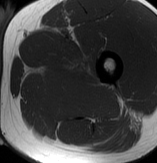
MRI of an extremity soft-tissue mass, one axial slice. Position 52 of 70 along the scan axis. MR volume resampled by the dataset authors to the PET/CT grid (not the native acquisition matrix). 3.27 mm slice thickness. 157 × 163 image matrix. Male patient. From the clinical record (not read from this slice): histological type: extraskeletal osteosarcoma; grade: high; site of the primary tumour: left adductur.
Structures marked on this image (expert contour drawn on MRI and transferred to this co-registered scan by the dataset authors):
- gross tumour volume (mass): bounding box (x1, y1, x2, y2) in pixels: (31, 55, 121, 121)